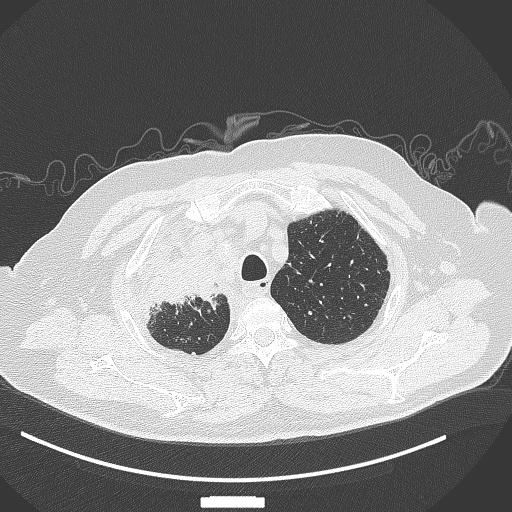
Chest CT, one axial slice; slice 309 of 384 in the series (ordered by position); reconstruction kernel B70f; lung window (W 1500 / L -600 HU); 1 mm slice thickness; 512 × 512 image matrix. Patient: male, 69 years. Case-level facts recorded for this patient, not image findings: clinical TNM (as recorded): T4 N3 M1.
Structures marked on this image (bounding box drawn by a radiologist):
- lung tumour (recorded histology: adenocarcinoma): bounding box (x1, y1, x2, y2) in pixels: (152, 264, 228, 314)